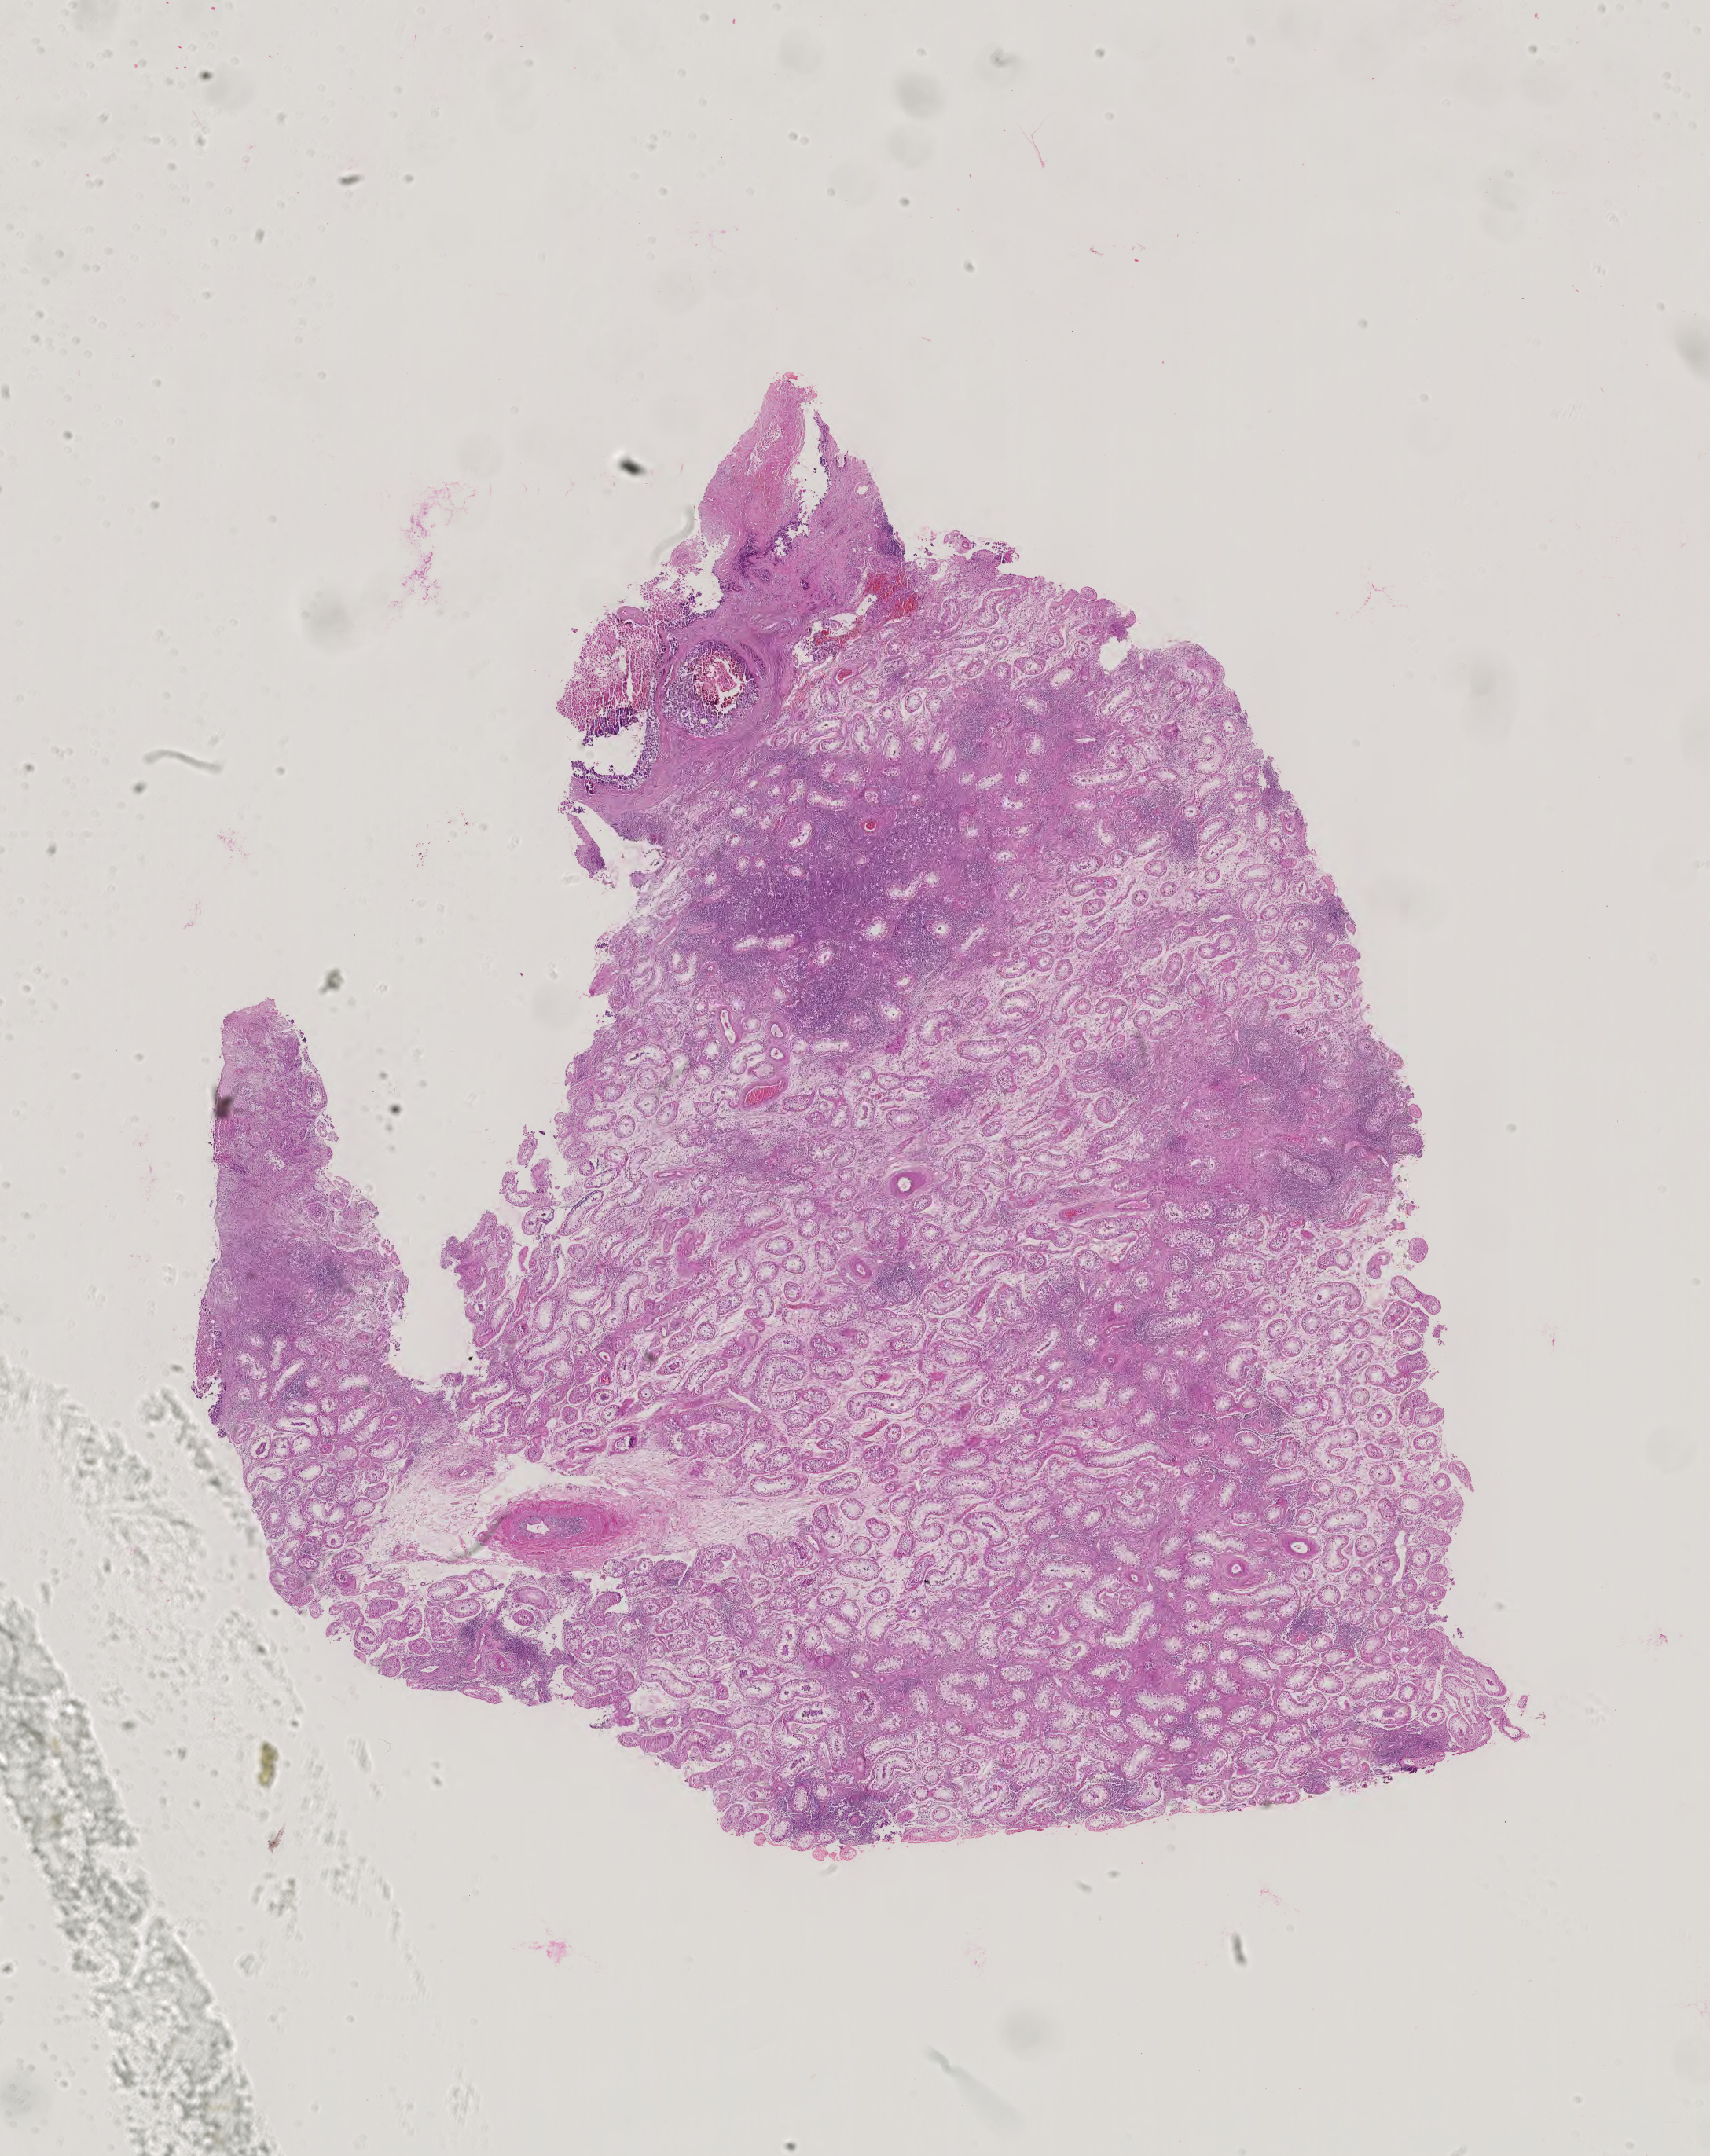
Digitized Hematoxylin and eosin (H&E) stained tissue section (whole slide) — a low-resolution overview of the entire scanned area, about 15.9 x 20.0 mm (slide scanned at 40x); FFPE section; sample: primary tumour, testis. Male, age 19 years at initial diagnosis.
Laterality: right. Histologic diagnosis: Embryonal carcinoma, NOS. AJCC pathologic stage: II (4th edition).